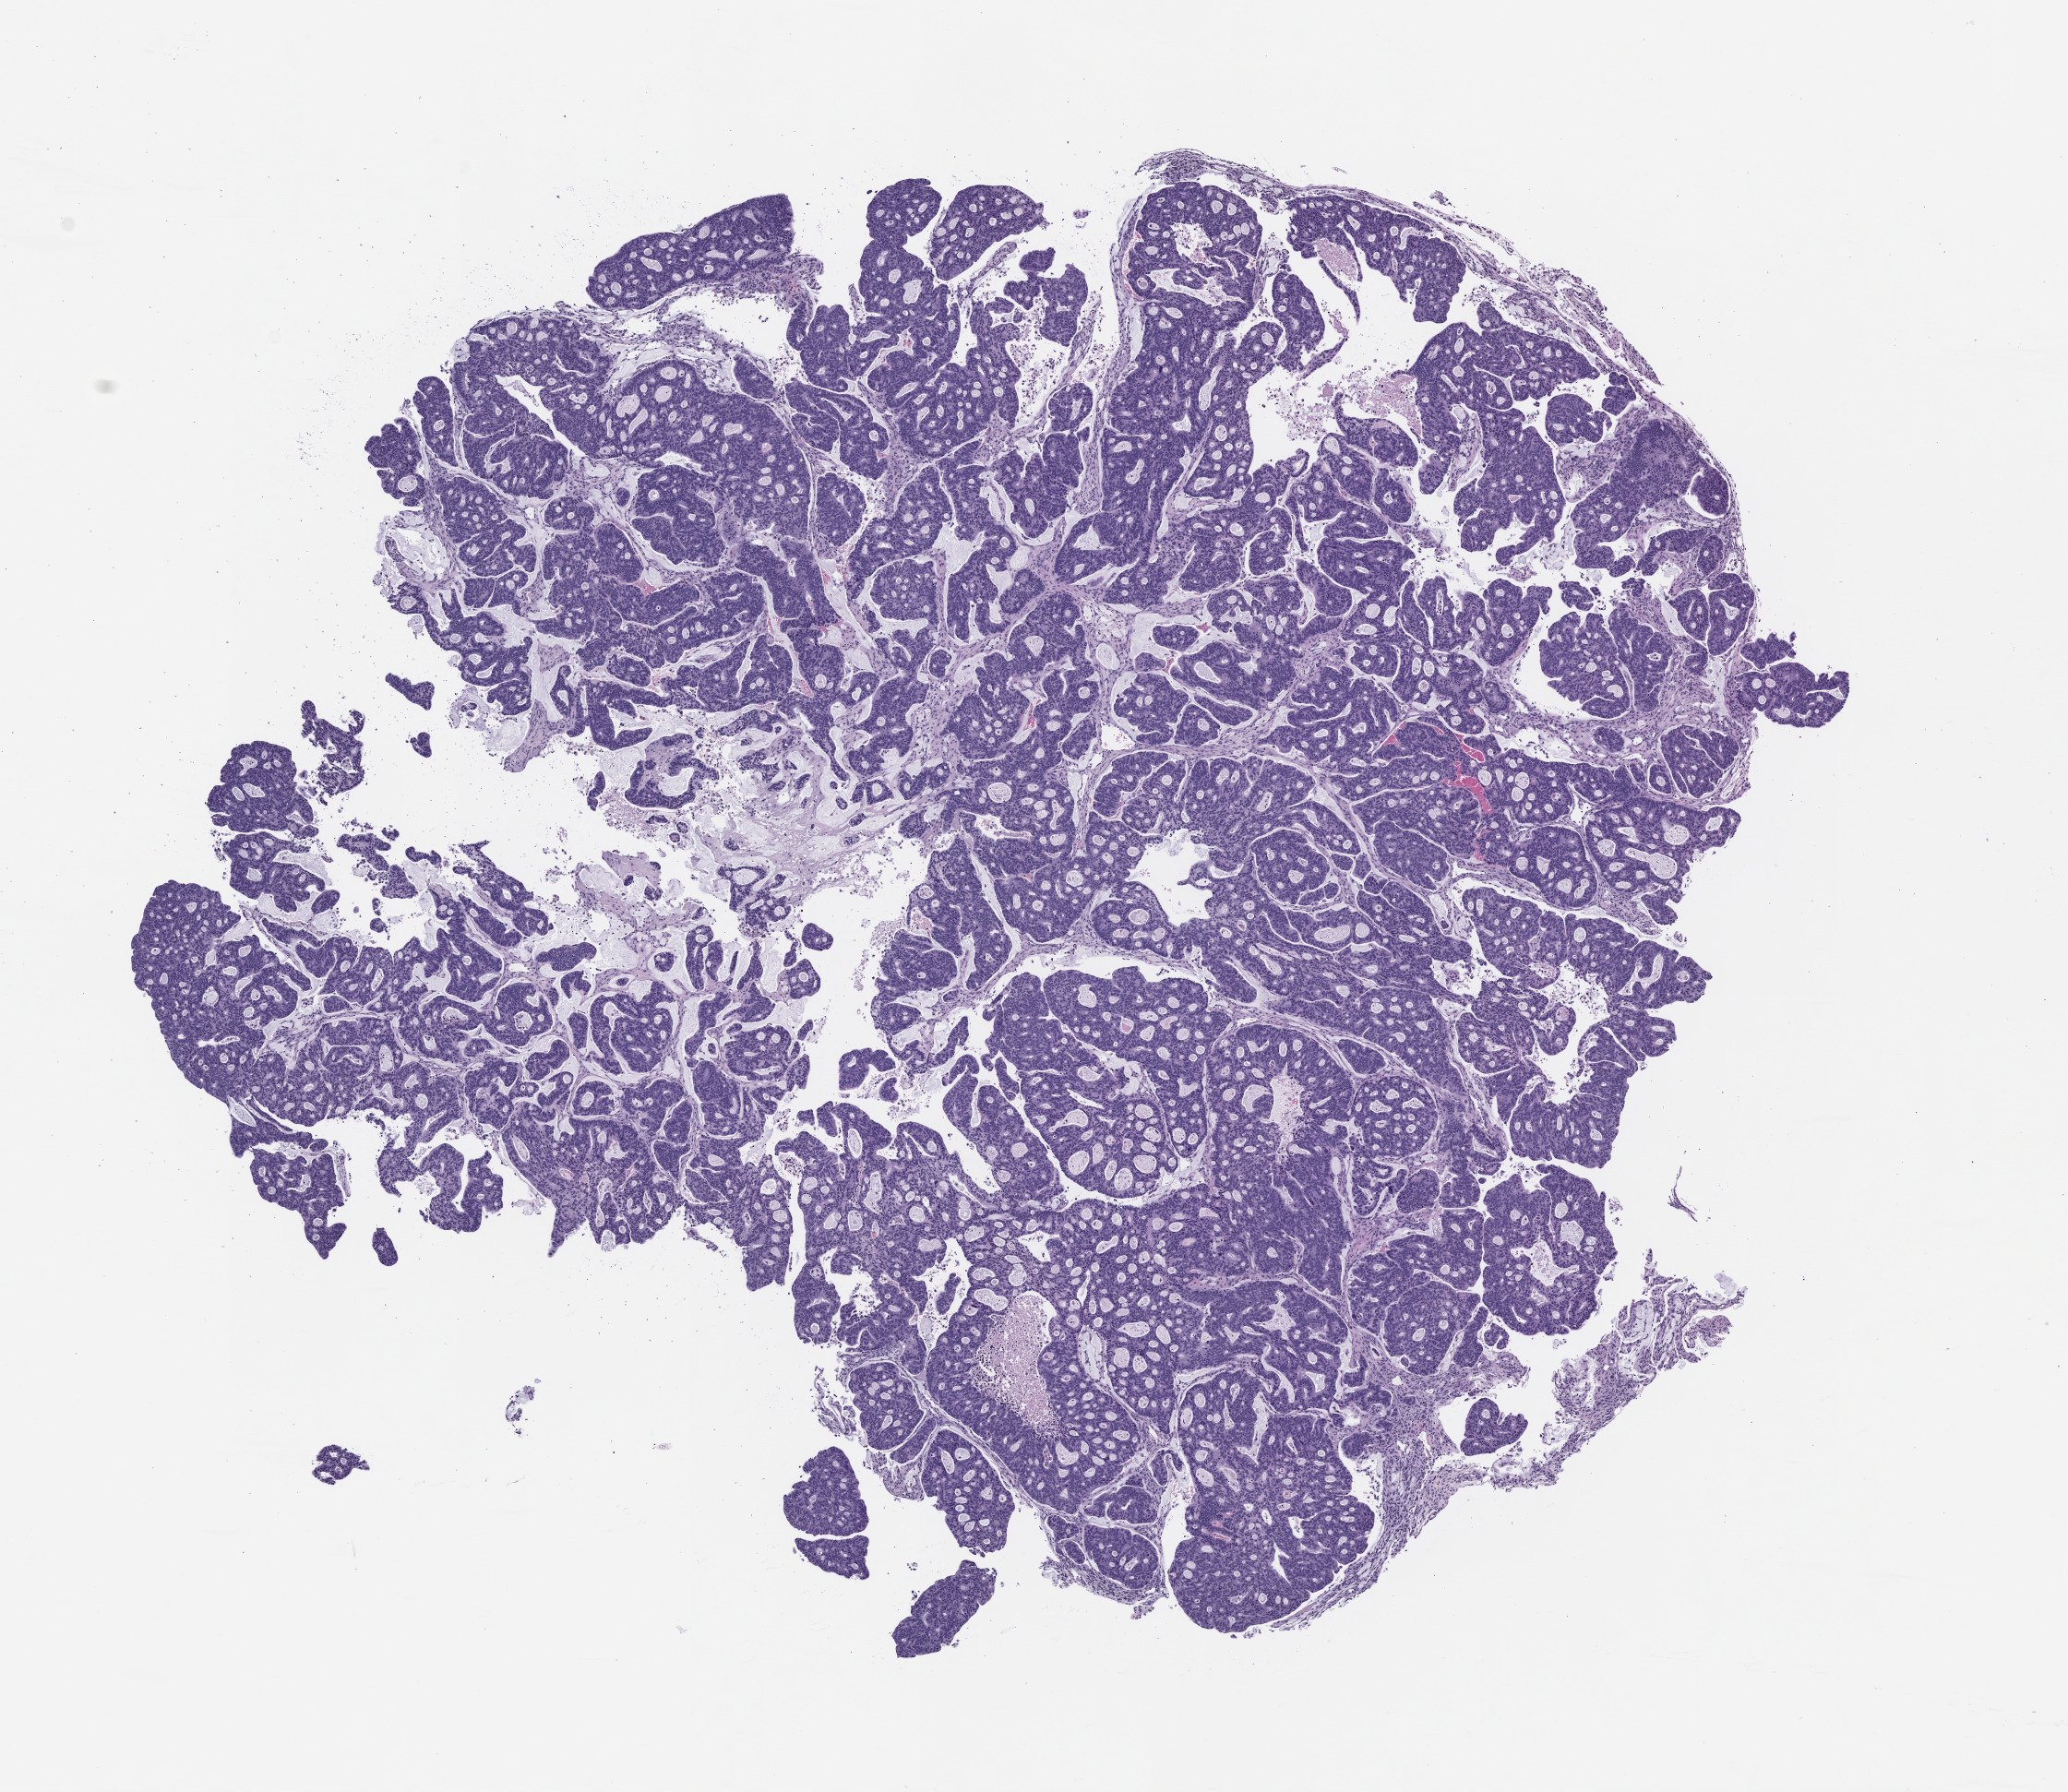
Whole-slide image, H&E: patient-derived xenograft (human tumor grown in a mouse), passage 1, shown as a low-resolution overview of the whole scanned area (about 9.0 x 7.8 mm). FFPE section. Originating tumor site category: colon.
• originating patient diagnosis: Colon Adenocarcinoma